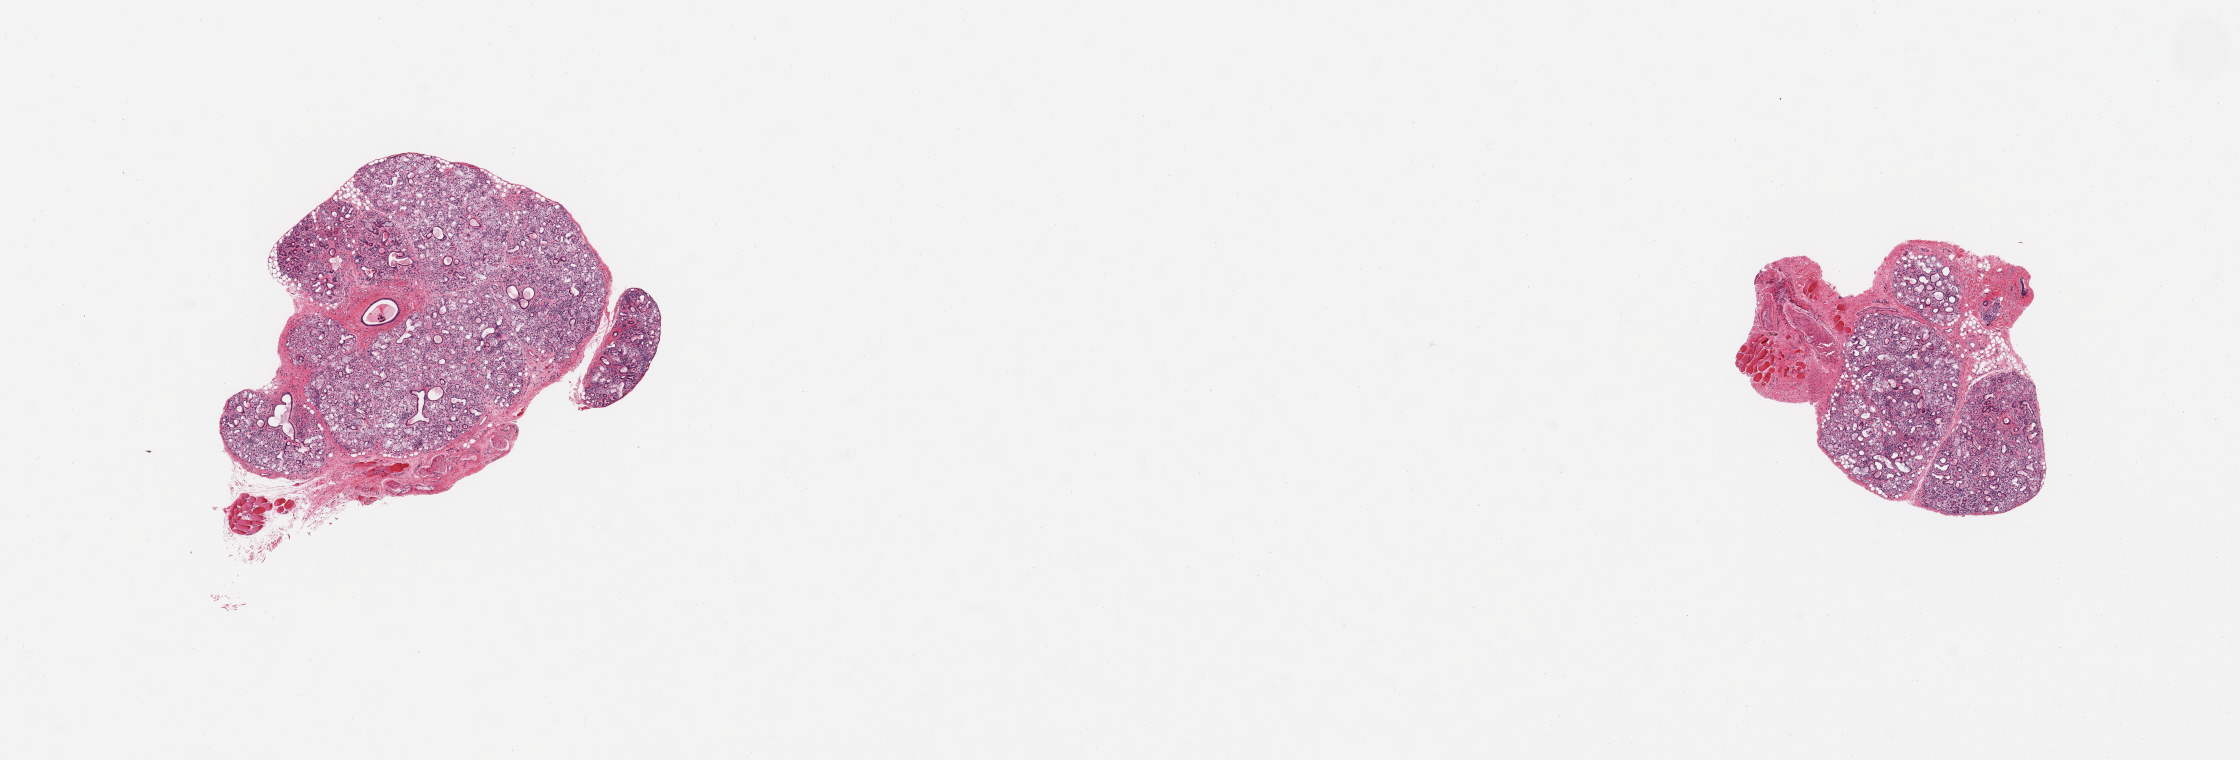
Digitized H&E-stained section — low-resolution overview of the scanned area, about 17.7 x 6.0 mm (from a 20x scan); PAXgene-fixed, paraffin-embedded tissue; sampled site (target tissue): breast; donor tissue sample. Donor sex: male.
Pathologist's review note for this sample: 2 pieces, minor salivary gland tissue.